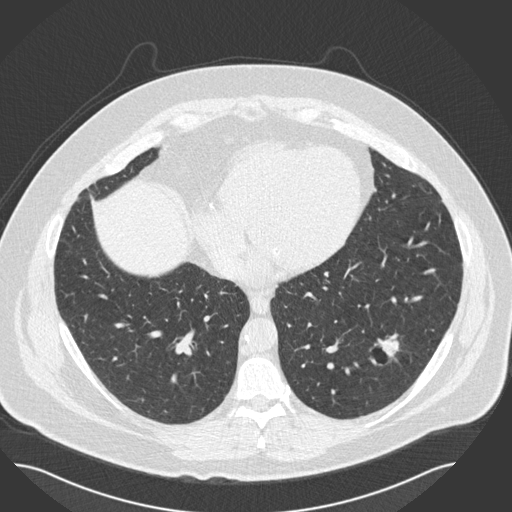
Low-dose screening chest CT, axial slice, second annual screen, lung window (W 1500 / L -600 HU), 2 mm slice thickness, standard (soft-tissue) reconstruction kernel (B30f), 120 kVp, slice 92 of 162 in the series. Male participant, aged 57 years at enrolment. Current smoker at enrolment.
- Expert-annotated lung lesion, bounding box <352,325,418,379> (left, top, right, bottom; pixels).
- Reader record for this screening exam (exam-level; its link to the box is not recorded): non-calcified nodule or mass ≥4 mm, left lower lobe, 19 × 15 mm, pre-existing on the prior screen: yes; interval growth: no.